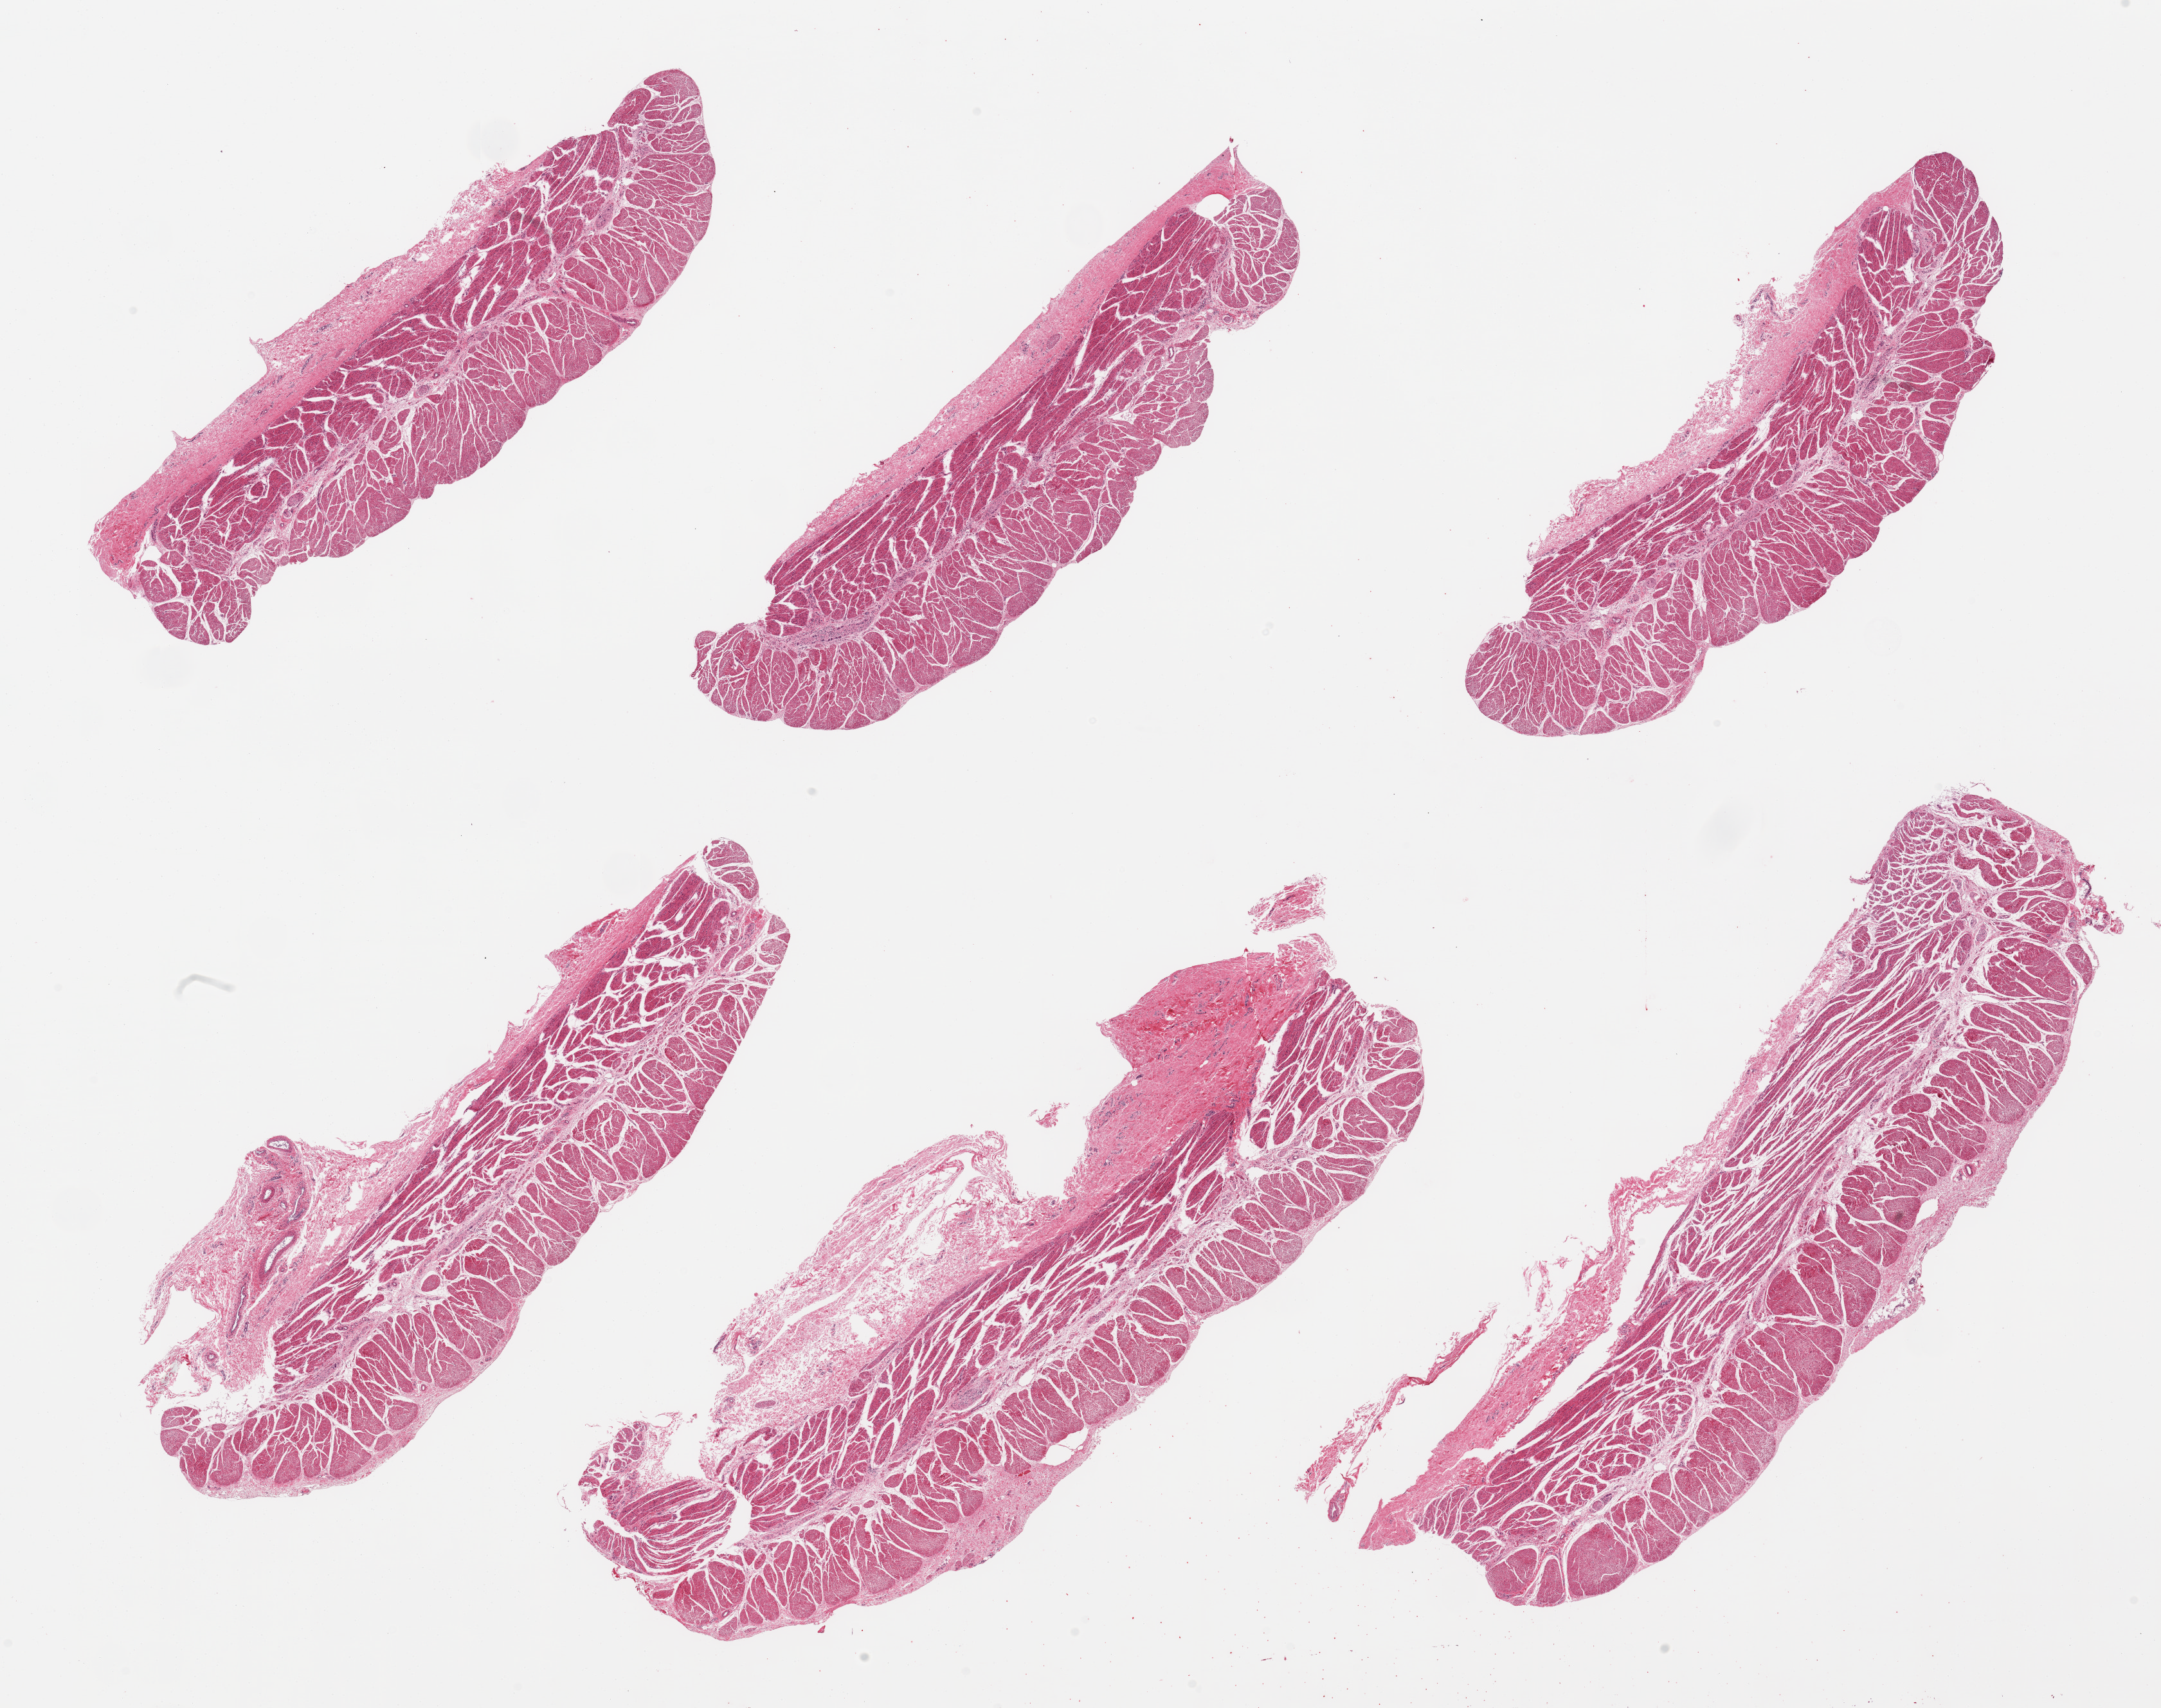
Whole-slide image, H&E stain, low-resolution overview of the scanned area, about 26.6 x 21.0 mm (from a 20x scan). PAXgene-fixed paraffin-embedded (PFPE) section. Section of esophageal muscle (target tissue). Donor tissue sample. Donor: male.
Review note (as recorded): 6 pieces; some residual attached fibrous/vascular tissue.